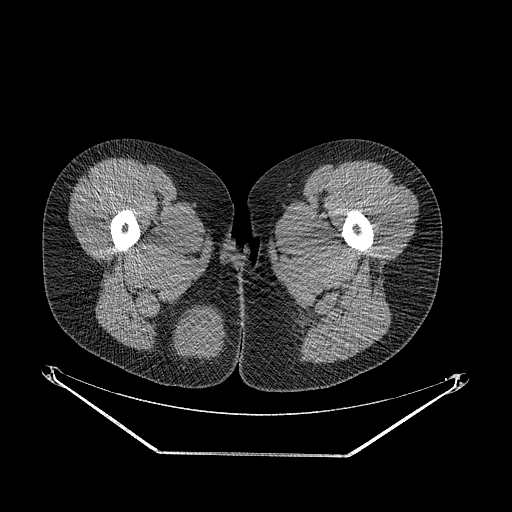
CT of an extremity soft-tissue mass (from a PET/CT study), one axial slice; position 23 of 267 along the scan axis; reconstruction kernel STANDARD; soft-tissue window (W 400 / L 40 HU); 512 × 512 image matrix, field of view 500 × 500 mm. Female patient. Case-level facts recorded for this patient, not image findings: histological type: epithelioid sarcoma; grade: intermediate; site of the primary tumour: right buttock.
Annotated regions visible in this slice (expert contour drawn on MRI and transferred to this co-registered scan by the dataset authors):
- gross tumour volume including surrounding oedema: box from (x=169, y=302) to (x=227, y=369) px
- gross tumour volume (mass): (x=174, y=308)–(x=225, y=359)